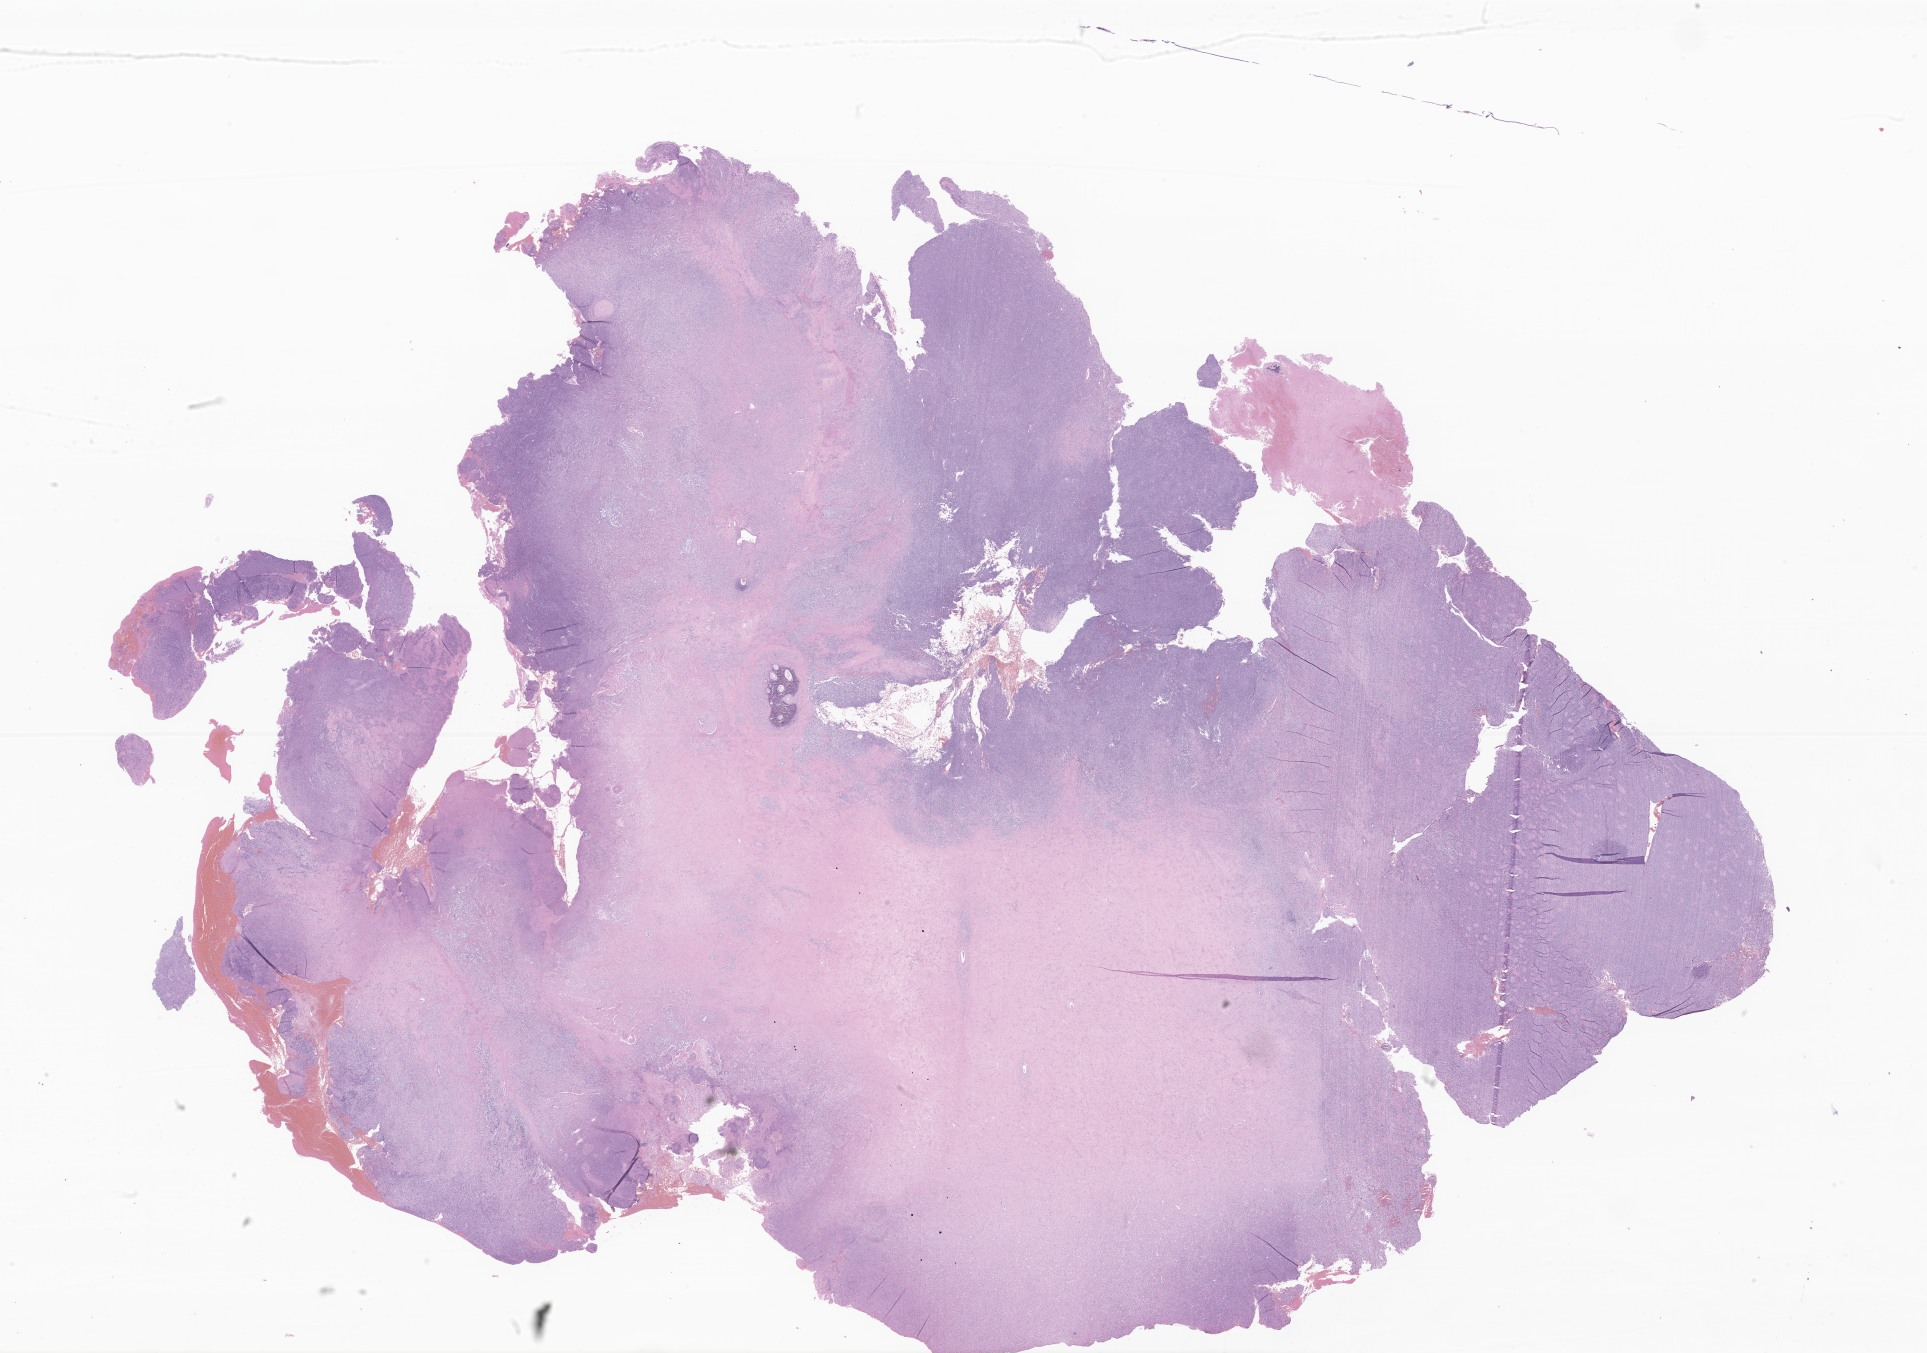
Whole-slide image, hematoxylin and eosin (H&E) stain of tumor tissue from the brain, whole scanned area (about 32.5 x 22.8 mm) shown as a low-resolution overview, FFPE section. Patient male; age 72 months (6 years).
* diagnosis: Neoplasm, uncertain whether benign or malignant